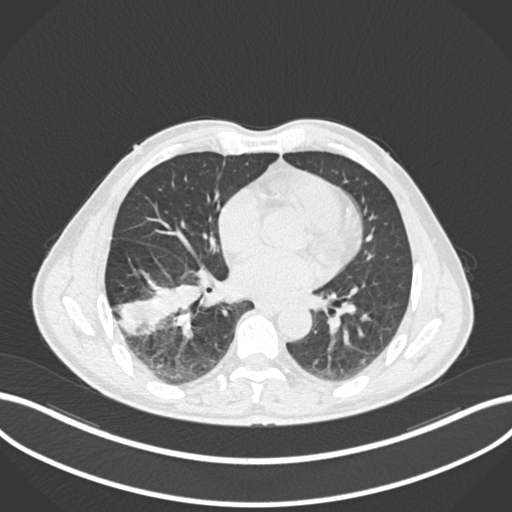
Chest CT, one axial slice; position 83 of 208 along the scan axis; reconstruction kernel B30f; lung window (W 1500 / L -600 HU); 1 mm slice thickness; 512 × 512 image matrix, field of view 400 × 400 mm. Patient: male, 58 years. Case-level facts recorded for this patient, not image findings: clinical TNM (as recorded): T3 N0 M0; histopathological grade: G2.
Structures marked on this image (rectangle marked by the reading radiologist):
- lung tumour (recorded histology: squamous cell carcinoma): bounding box <112,282,201,338> (left, top, right, bottom; pixels)